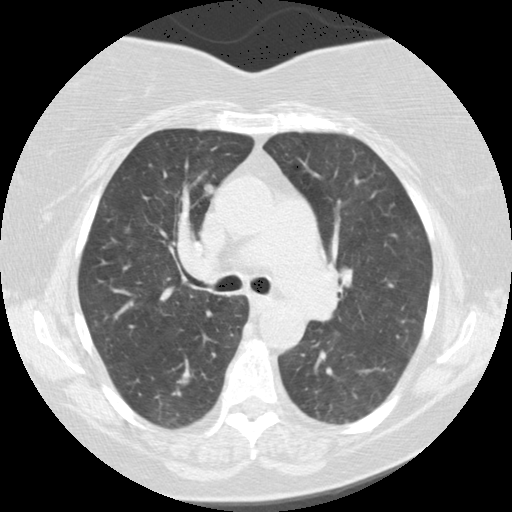
Low-dose screening chest CT, axial slice; second annual screen; lung window (W 1500 / L -600 HU); 512 × 512 image matrix. Female participant, aged 62 years at enrolment. Current smoker at enrolment.
Expert reader's lesion annotation, bounding box [x1, y1, x2, y2] px = [184, 169, 235, 210]. The screening reader recorded 3 non-calcified nodules or masses ≥4 mm on this exam (right lower lobe, right lower lobe, right lower lobe); which of them this box marks is not recorded. Participant outcome: lung cancer diagnosed 376 days after this screen (after the third annual screen) — adenocarcinoma, NOS, right upper lobe, poorly differentiated (G3), stage IB (AJCC 6th edition), 12 mm at pathology.